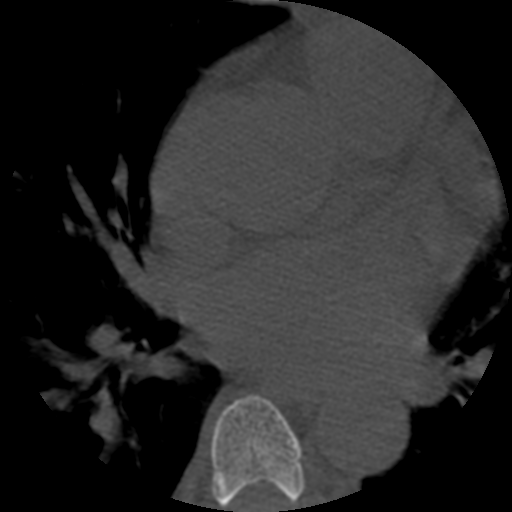
CT including the spine, one axial slice; reconstruction kernel STANDARD; bone window (W 1800 / L 400 HU); 1.25 mm slice thickness; 512 × 512 image matrix, field of view 160 × 160 mm. Patient age 57 years. From the clinical record (not read from this slice): primary cancer: prostate.
Annotated regions visible in this slice (semi-automatically segmented with operator editing):
- T6 vertebra: box from (x=211, y=395) to (x=306, y=512) px